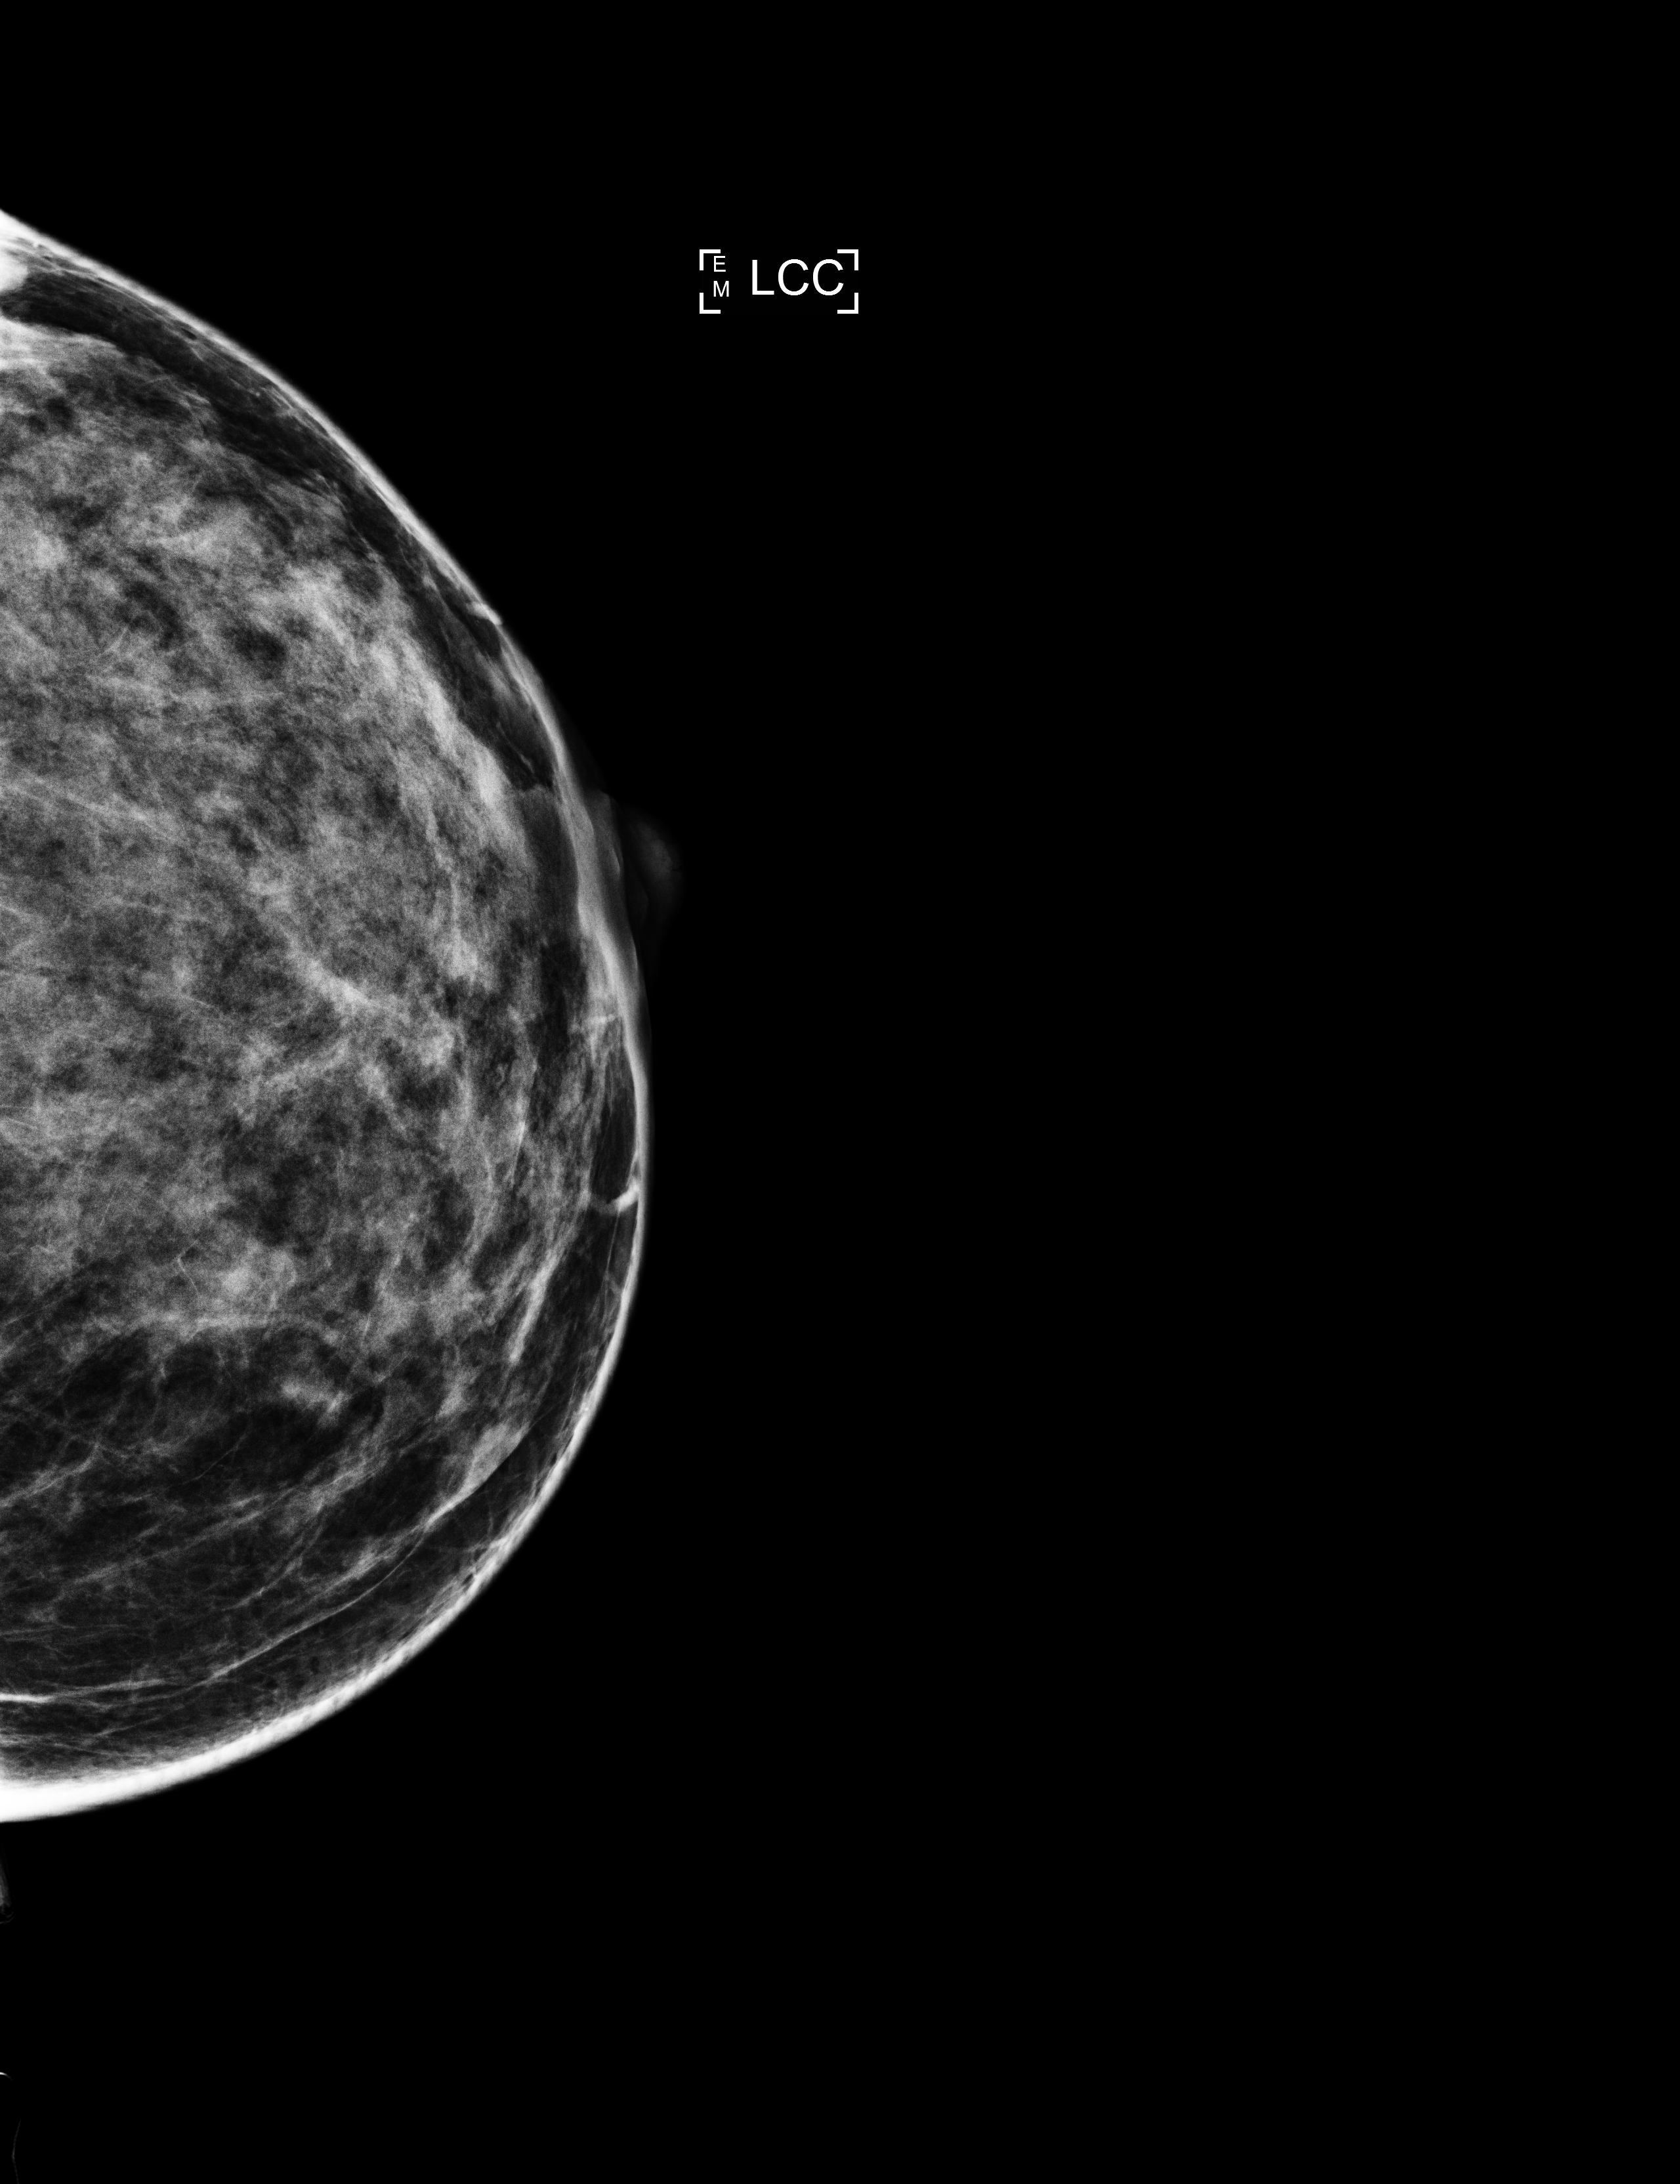
Annual screening mammography examination, compressed breast thickness 46 mm, system: Selenia Dimensions. Patient: female, 44 years.
Image type: full-field digital mammogram. Breast: left. Projection: craniocaudal (CC) view.